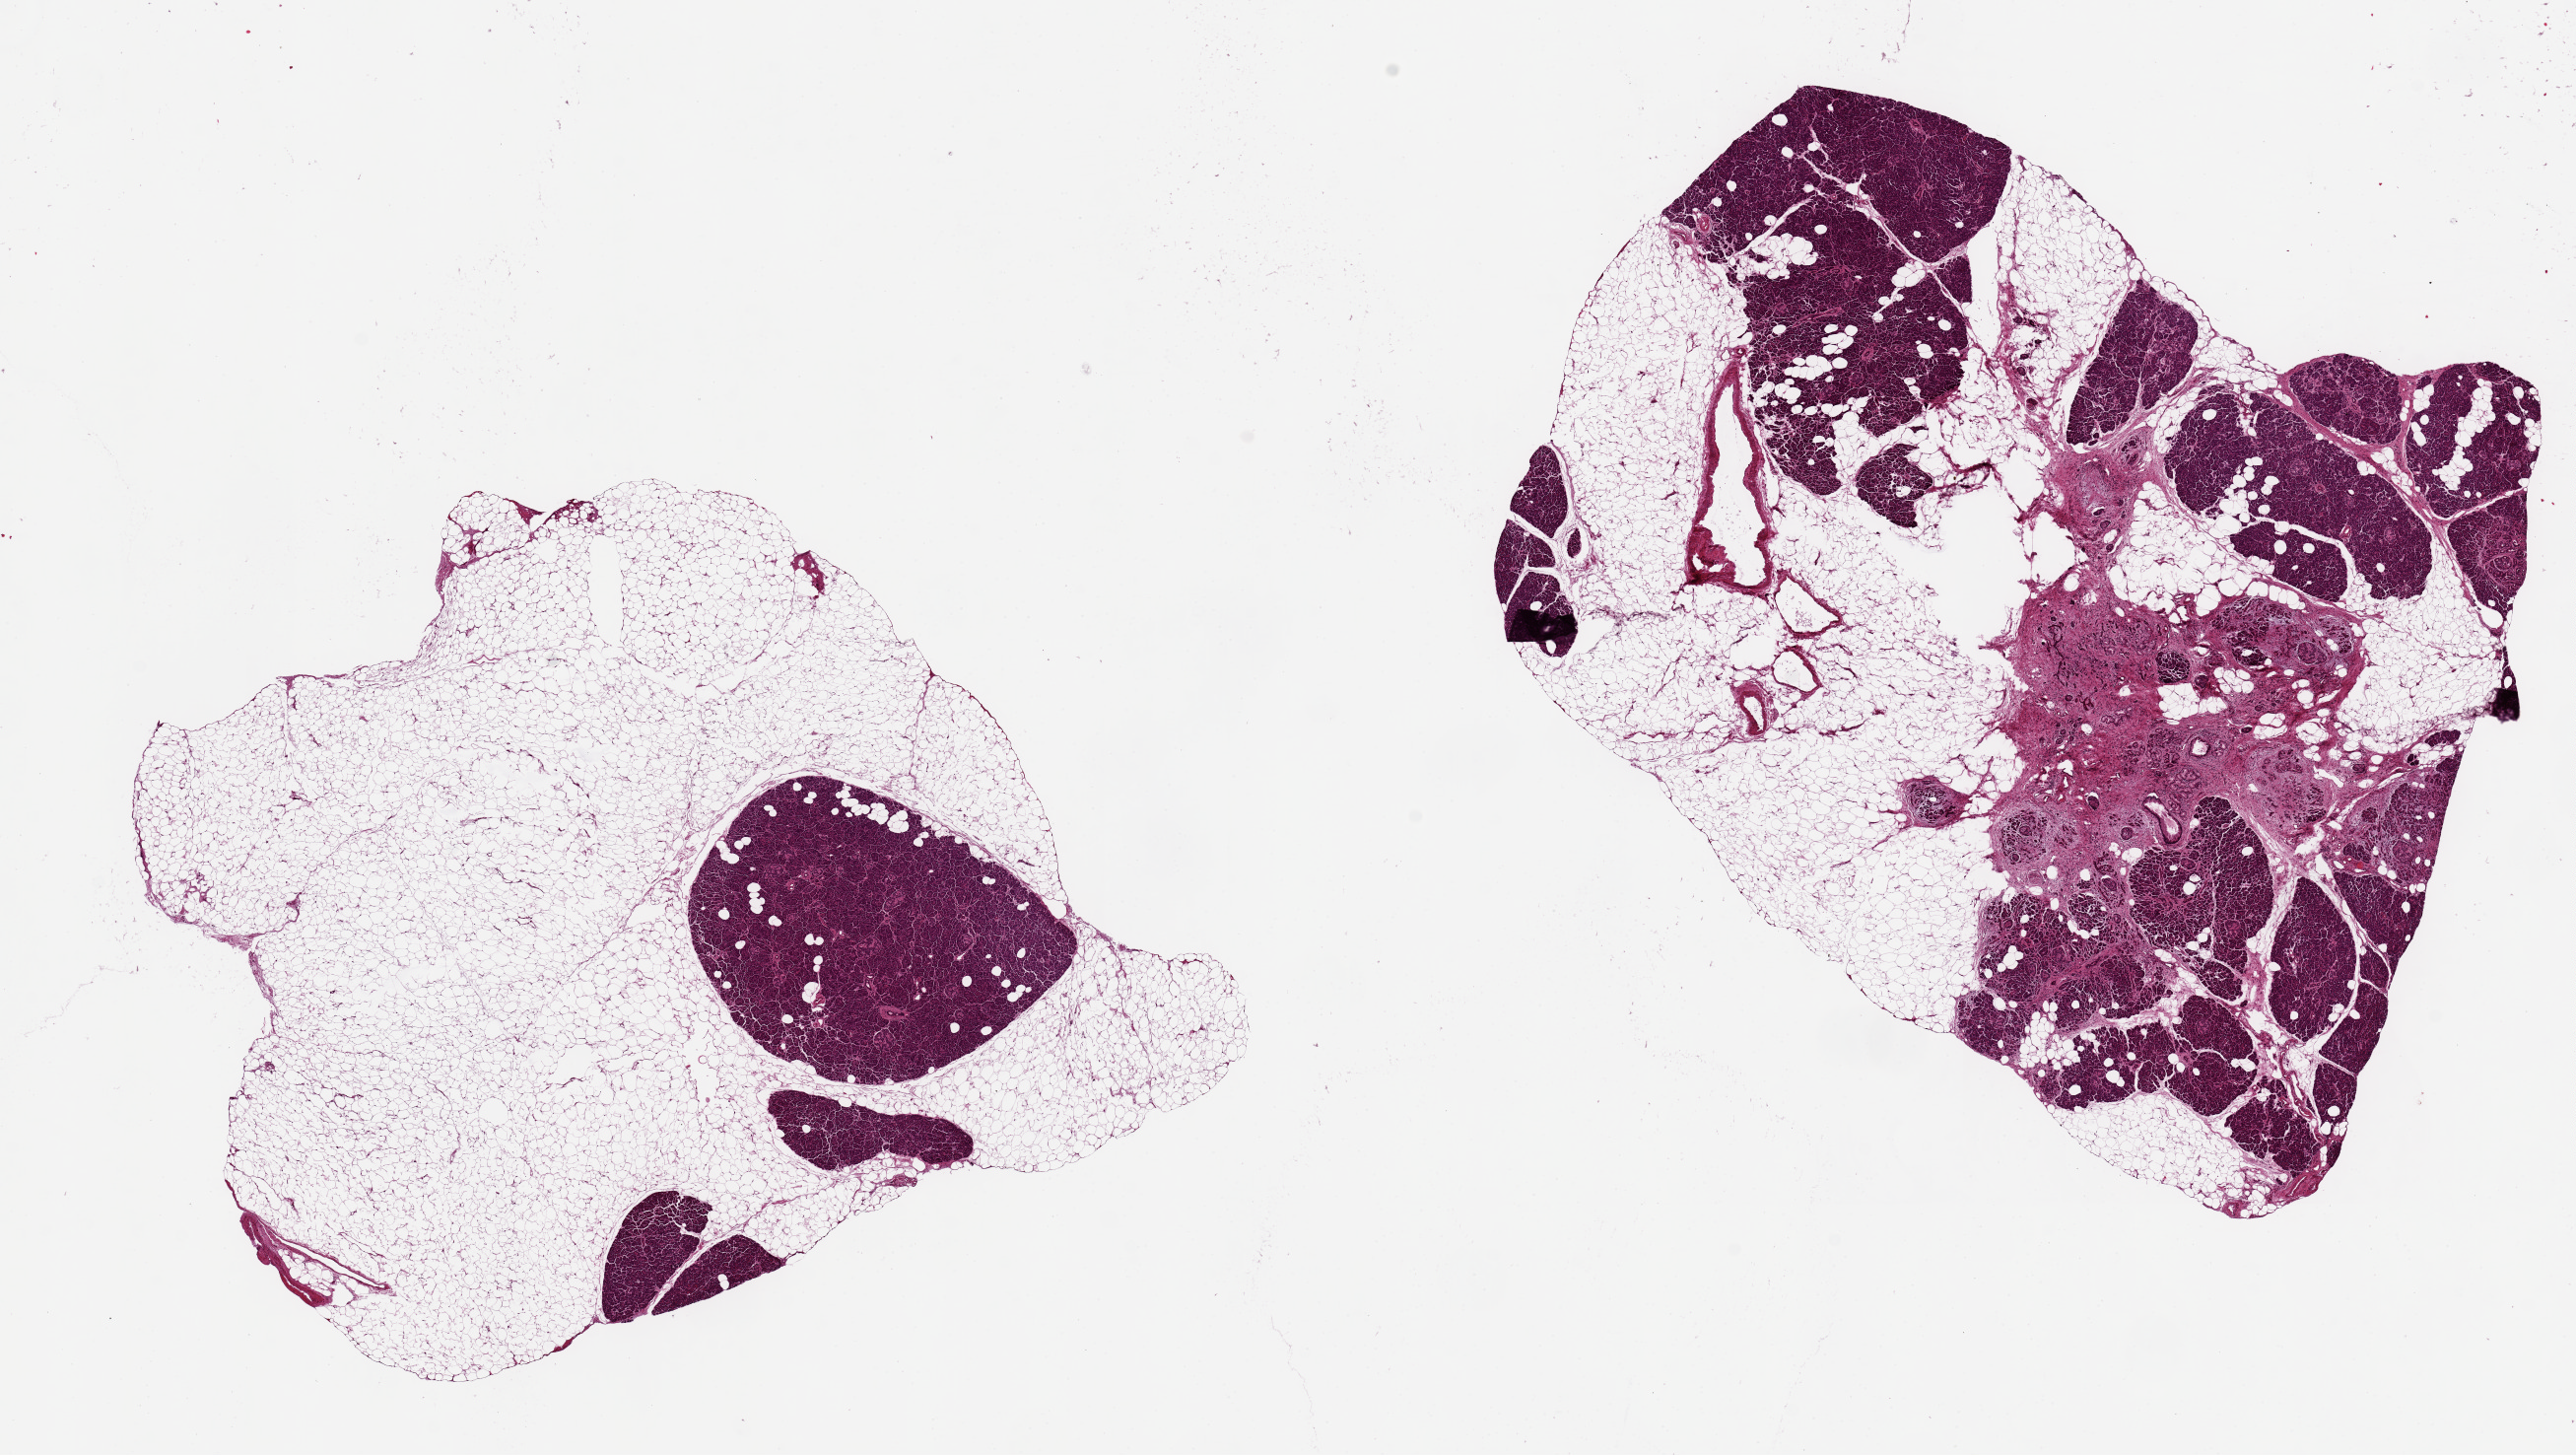
H&E whole-slide image — shown as a low-resolution overview of the whole scanned area (about 20.7 x 11.7 mm); PAXgene-fixed paraffin-embedded (PFPE) section; target tissue: pancreas; tissue donor sample. Donor sex: female.
Reviewer comment on this tissue sample: 2 pieces 8x7 & 7x6 mm; larger has ~20% scarring, 30% parenchyma, and 50% adipose: smaller is ~80% adipose, 20% parenchyma.